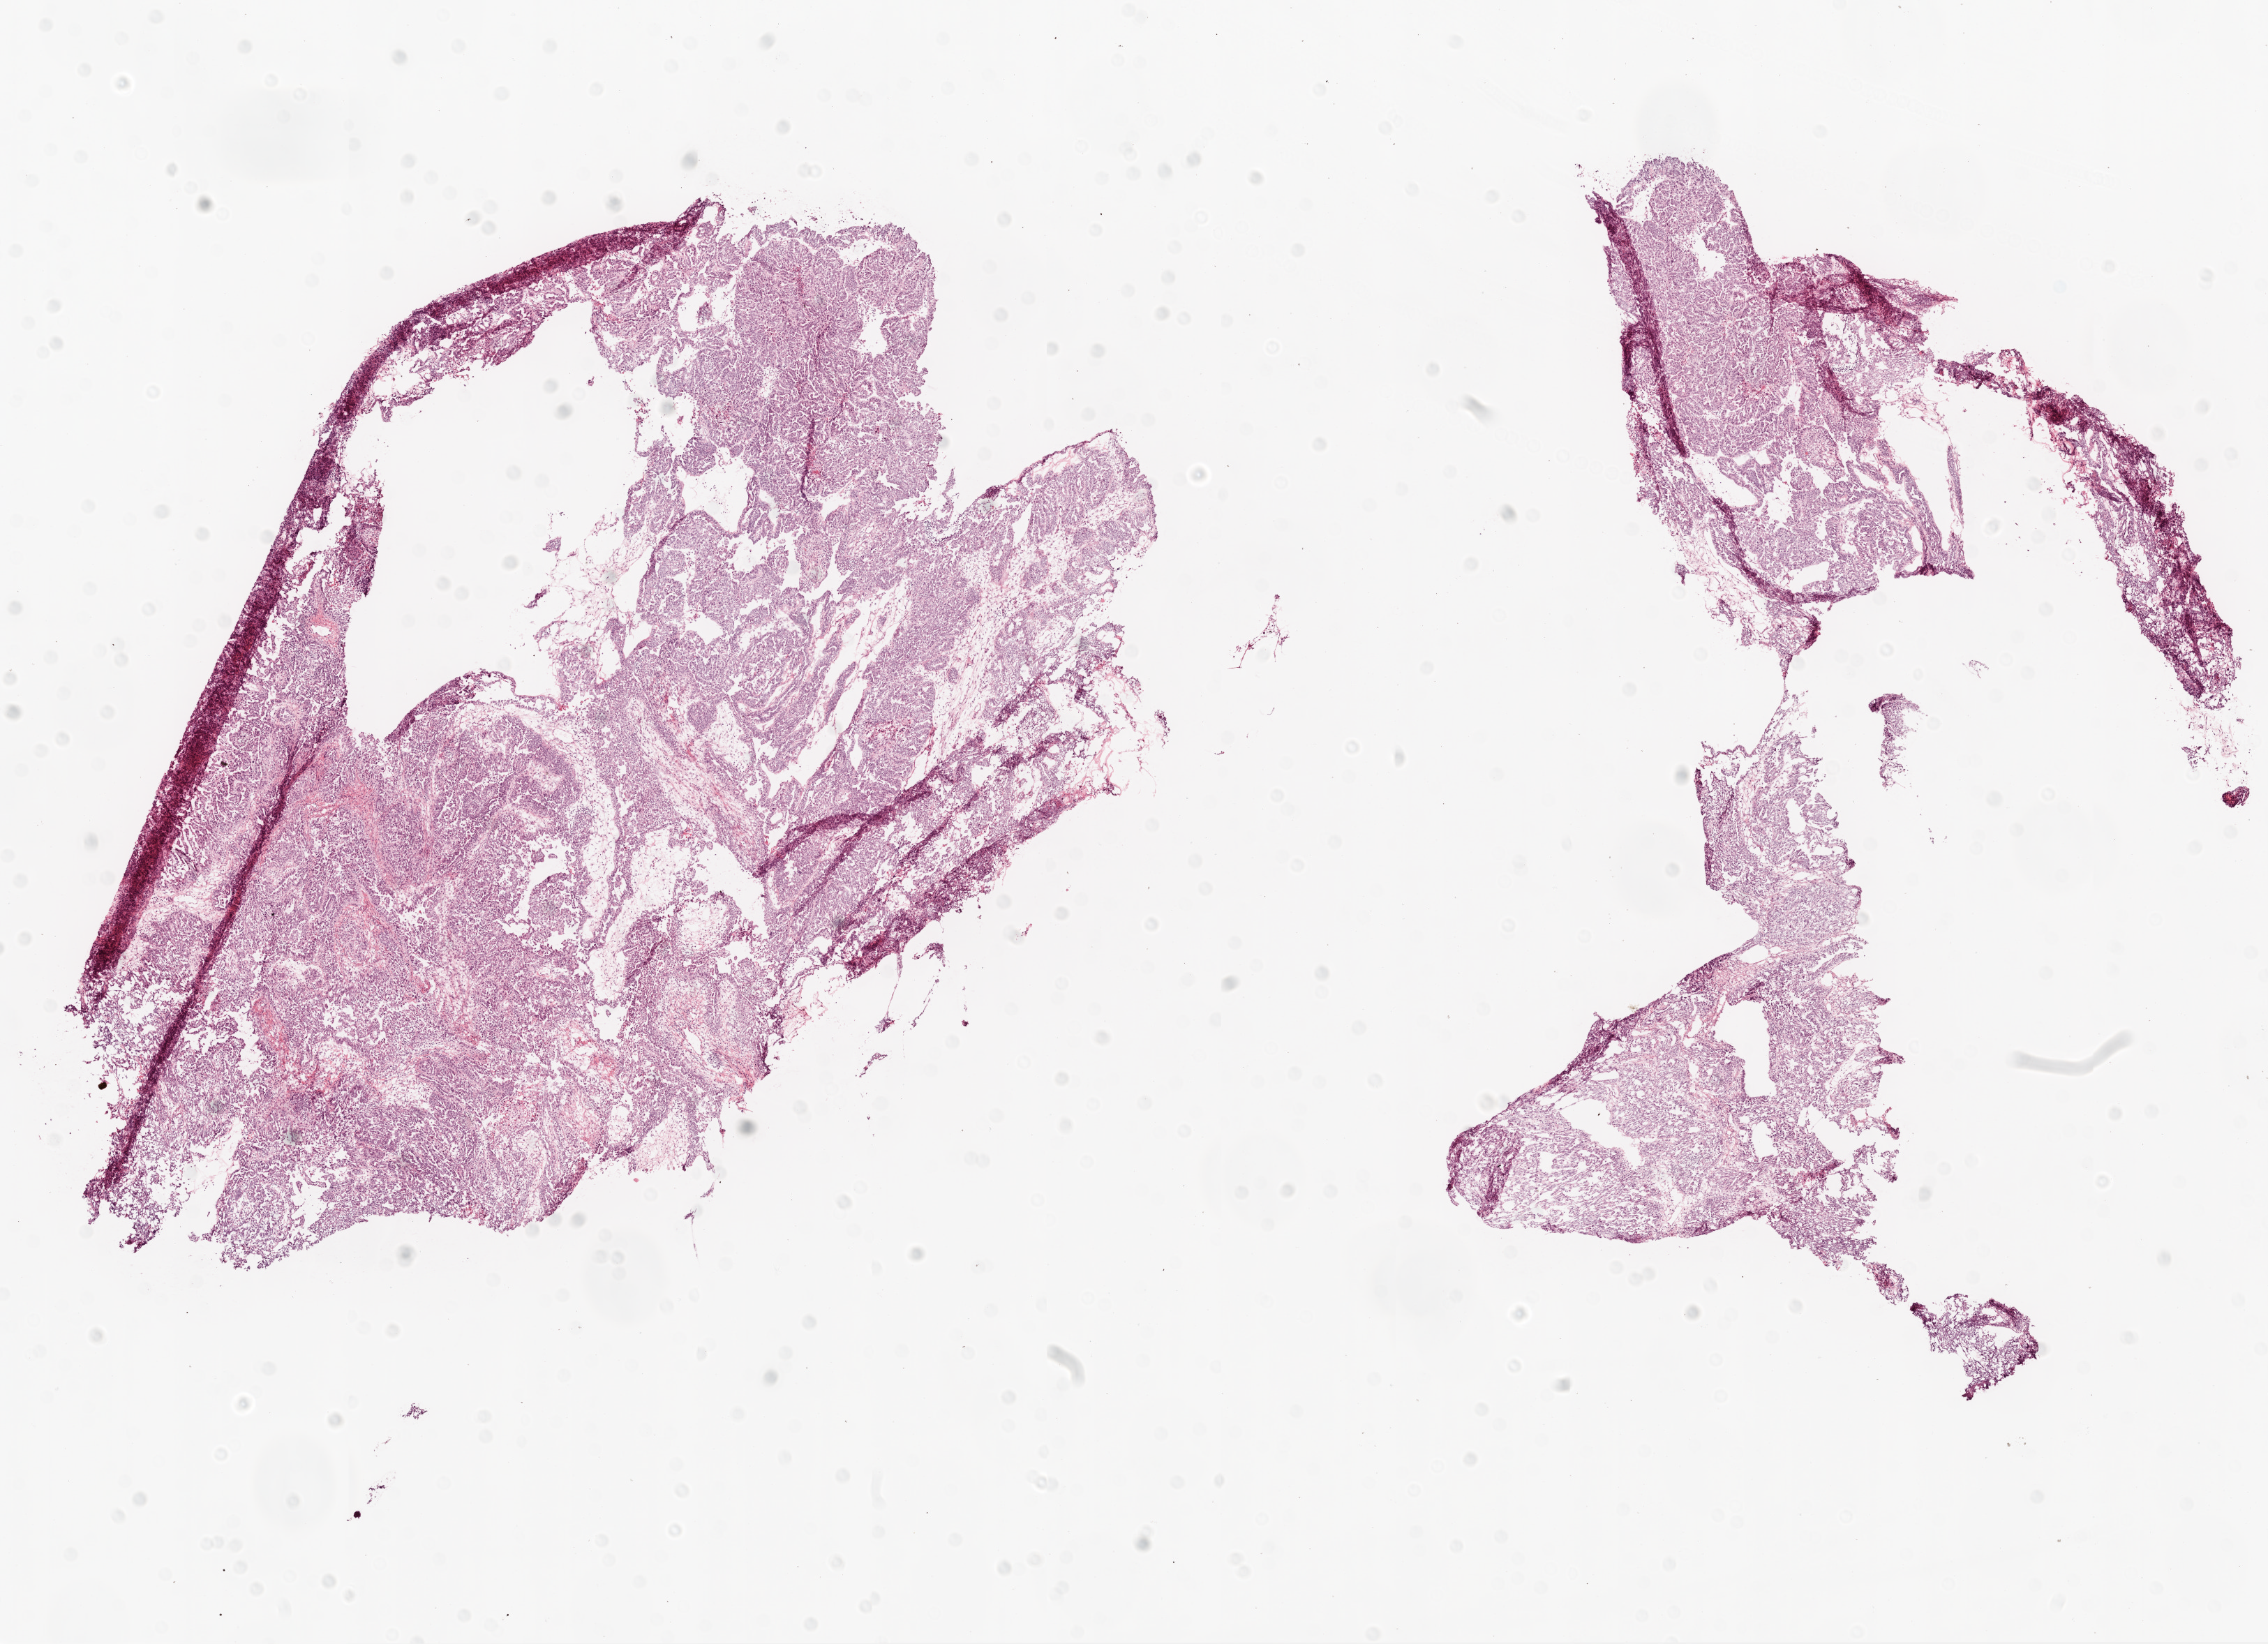
Whole-slide histology image, H&E, shown as a low-resolution overview of the whole scanned area (about 13.0 x 9.5 mm). Frozen section. Primary tumour sample from the ovary. Patient: female, age at initial diagnosis 62 years. Histologic grade: G3 (poorly differentiated). Pathologist review of this section (percent, as recorded): tumour cells 75%, tumour nuclei 80%, normal cells 0%, stromal cells 25%, necrosis 0%.
FIGO stage: IC. Diagnosis: Serous cystadenocarcinoma, NOS.